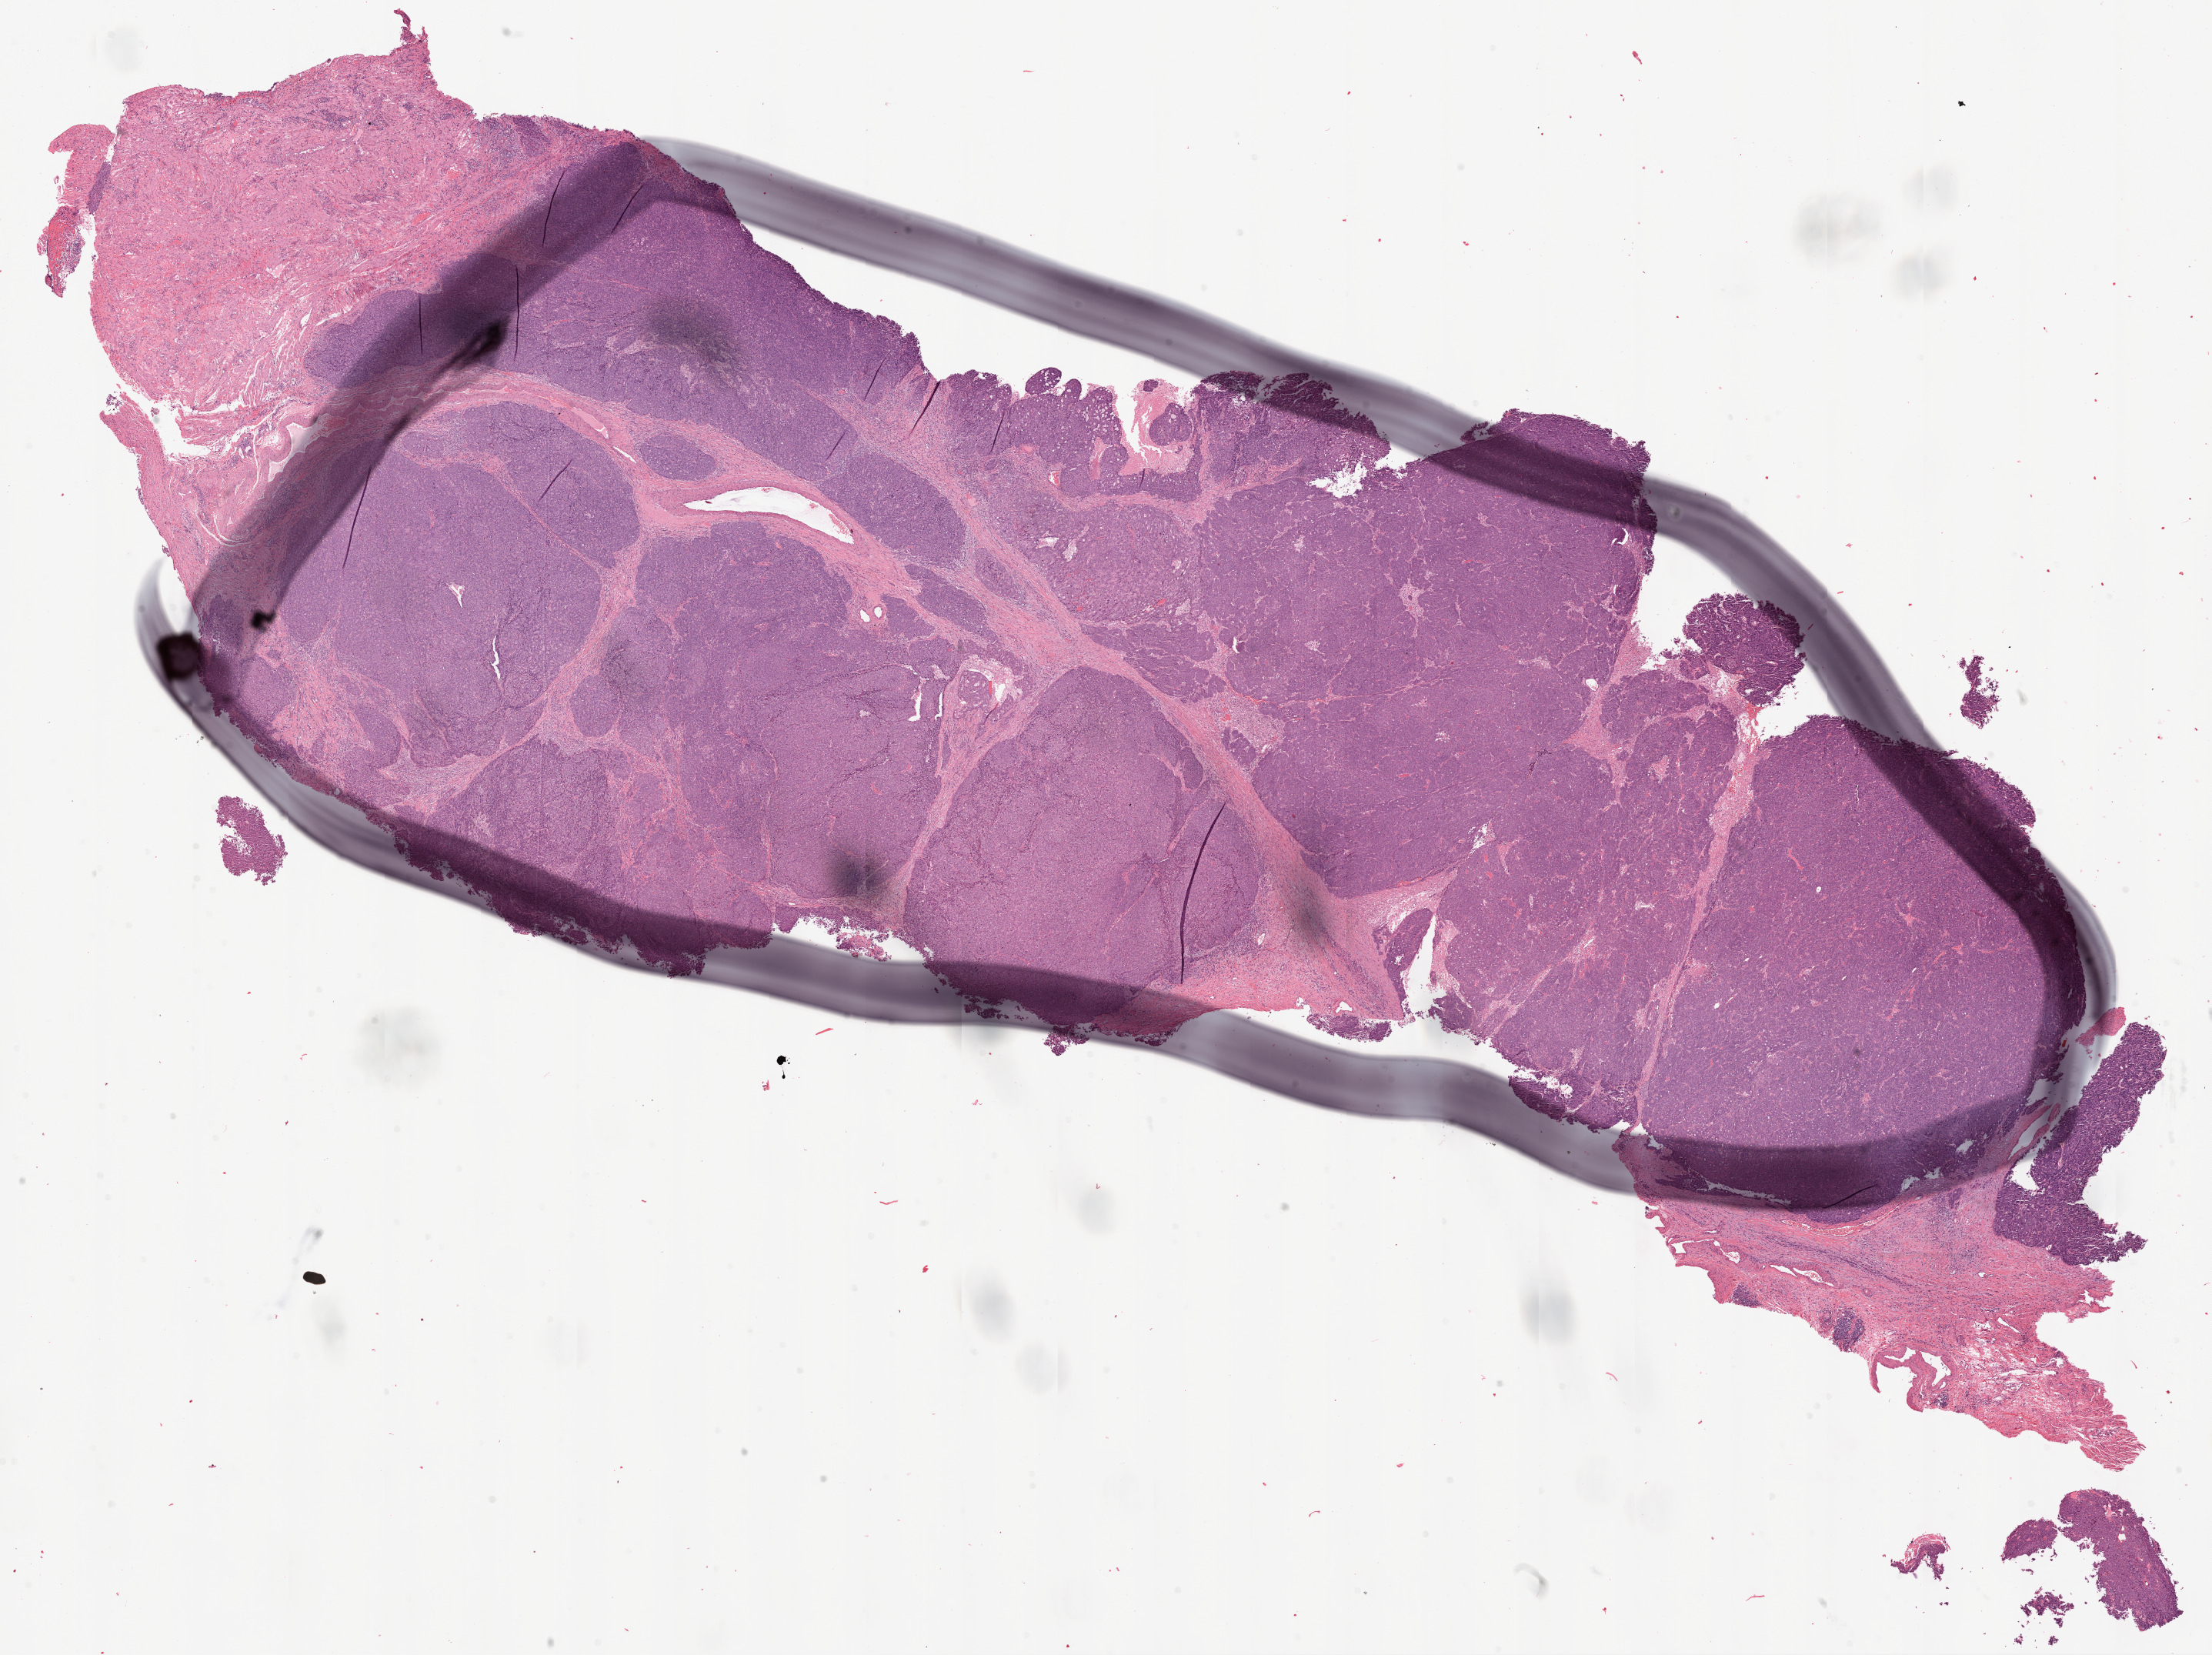
H&E-stained whole-slide image — a low-resolution overview of the entire scanned area, about 23.1 x 17.3 mm (acquisition: 20x scan). Frozen section from the top of the tissue portion. Ovary, primary tumour sample. Female, age 72 years at initial diagnosis. Histologic grade: G3 (poorly differentiated). Pathologist review of this section (percent, as recorded): tumour cells 83%, tumour nuclei 85%, normal cells 0%, stromal cells 15%, necrosis 2%.
Histologic diagnosis: Serous cystadenocarcinoma, NOS. FIGO stage: IIIC. Laterality: right.